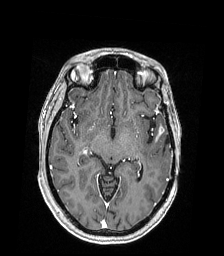
Brain MRI from a brain-tumour surgery series, one axial slice; position 109 of 168 along the scan axis; T1-weighted post-contrast; 1 mm slice thickness; 224 × 256 image matrix, field of view 224 × 256 mm. From the clinical record (not read from this slice): histopathology: Astrocytoma; WHO grade: 4; IDH mutation: yes; tumour location: Left Temporal.
Outlined on this slice (outlined manually by an expert reader):
- tumour: box from (x=151, y=123) to (x=166, y=139) px